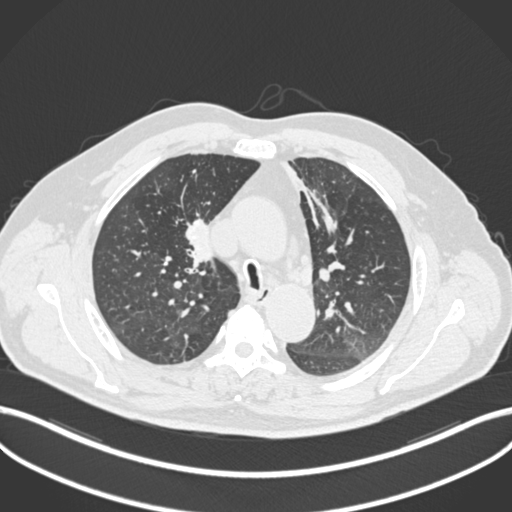
Chest CT, one axial slice; position 137 of 255 along the scan axis; 120 kVp; lung window (W 1500 / L -600 HU); 1 mm slice thickness; 512 × 512 image matrix, field of view 400 × 400 mm. Male patient, age 60 years. From the clinical record (not read from this slice): clinical TNM (as recorded): T1b N1 M0.
Structures marked on this image (rectangle marked by the reading radiologist):
- lung tumour (recorded histology: squamous cell carcinoma): box from (x=180, y=218) to (x=219, y=276) px